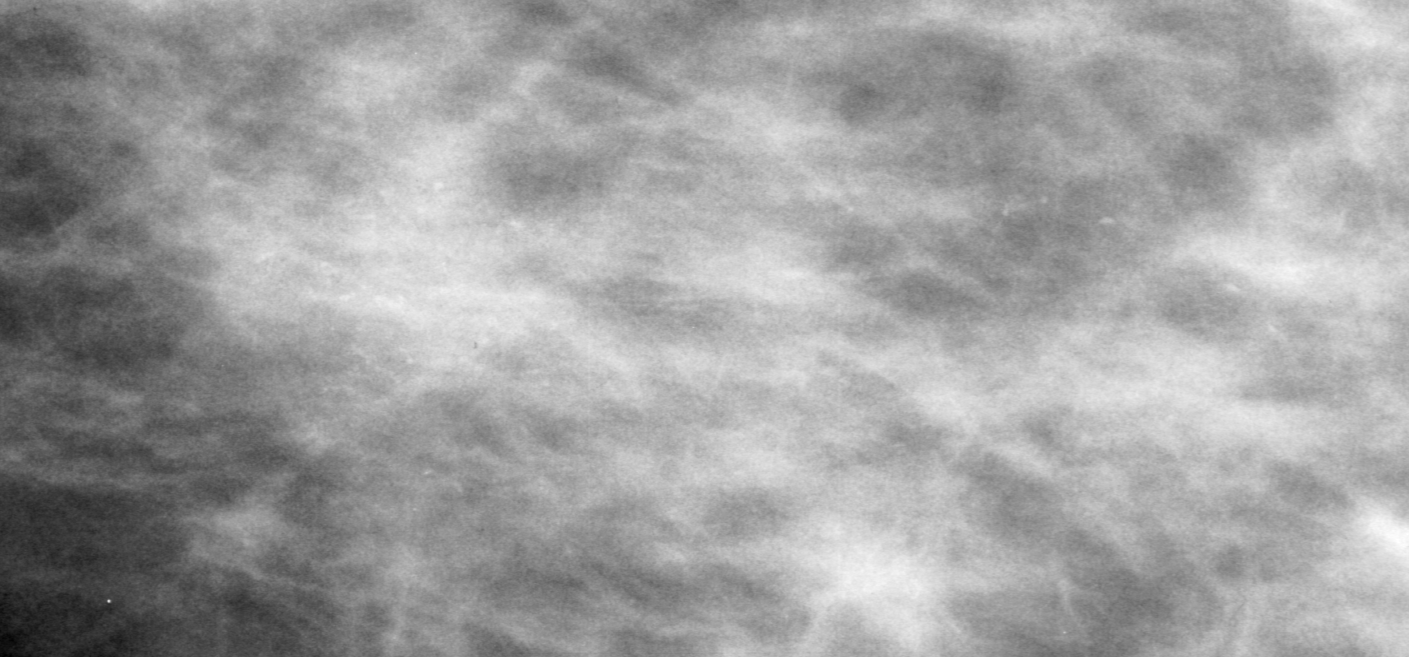
Region of interest cut from a scanned film mammogram (one marked finding); right breast; CC view.
Marked abnormality: calcifications, morphology pleomorphic, distribution segmental; BI-RADS assessment category 4; pathology result (as recorded, not read from the image): malignant.